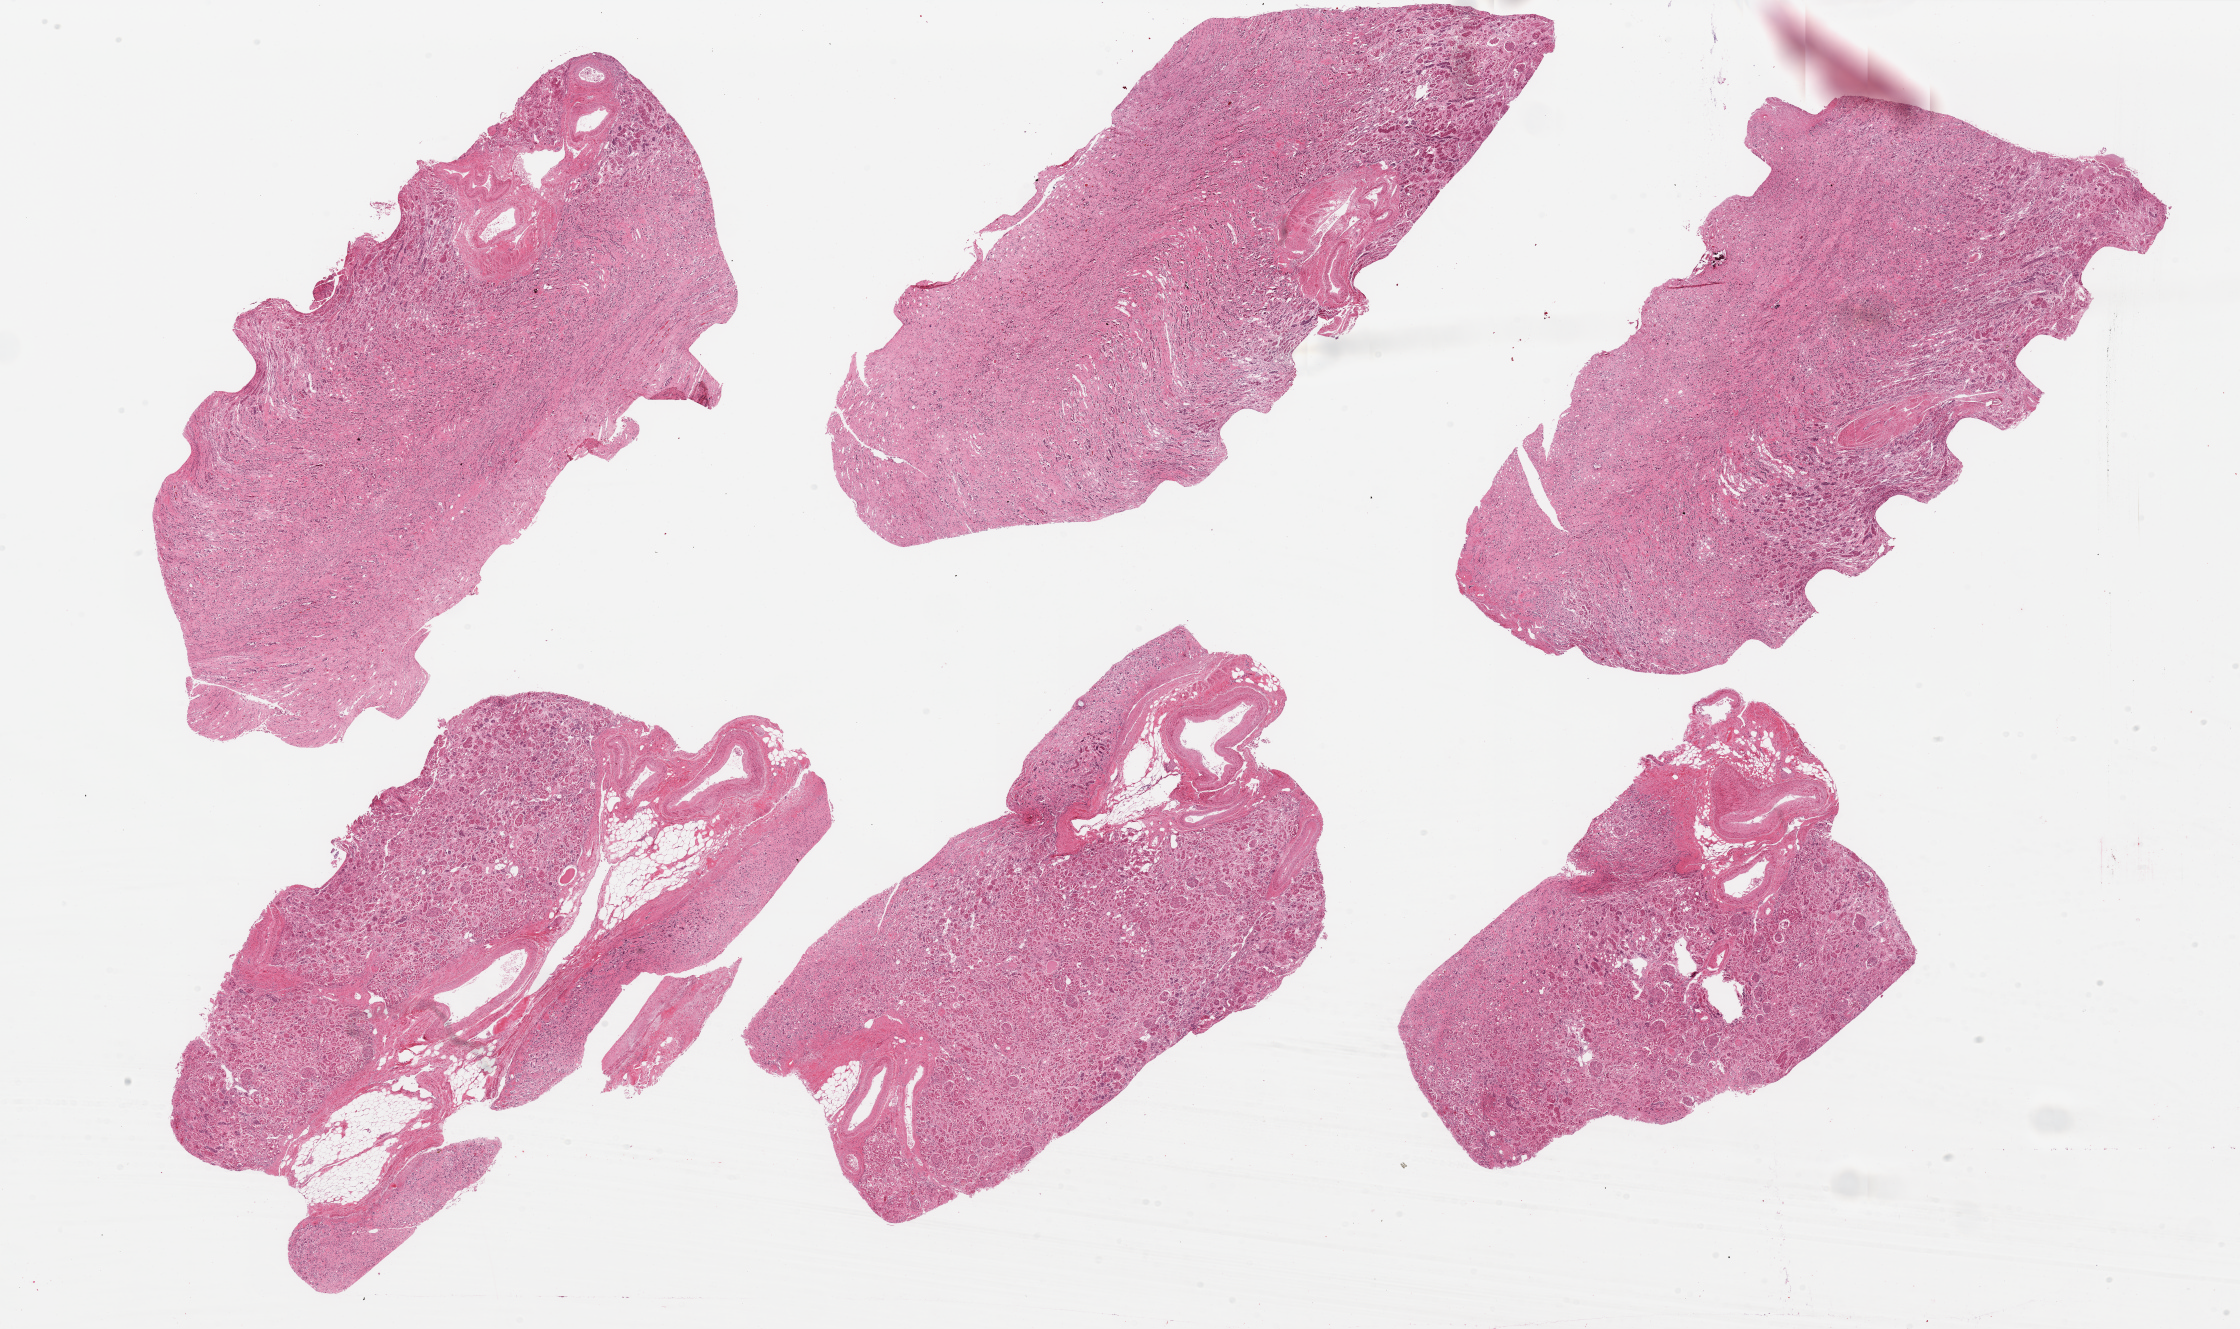
Digitized H&E-stained section — low-resolution overview of the scanned area, about 35.4 x 21.0 mm (acquisition: 20x scan); PAXgene-fixed, paraffin-embedded tissue; sampled site (target tissue): renal cortex; tissue donor sample.
Pathologist's review note for this sample: 6 pieces, 3 with glomeruli all with, advanced autolysis.